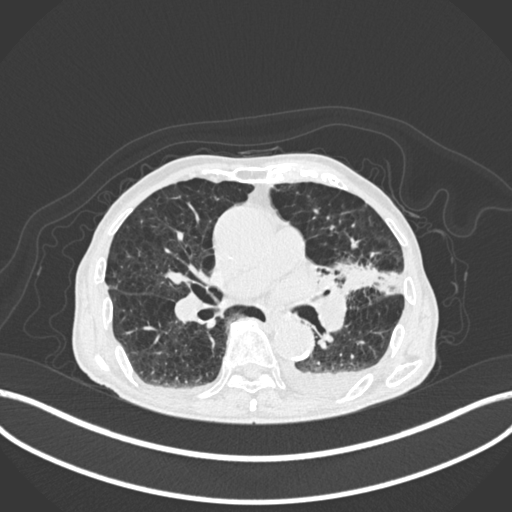
Chest CT, one axial slice; slice 116 of 400 in the series (ordered by position); lung window (W 1500 / L -600 HU); 512 × 512 image matrix. Male patient, age 90 years or older. Case-level facts recorded for this patient, not image findings: clinical TNM (as recorded): T2b N1 M0.
Annotated regions visible in this slice (rectangle marked by the reading radiologist):
- lung tumour (recorded histology: squamous cell carcinoma): bounding box (x1, y1, x2, y2) in pixels: (334, 261, 383, 291)